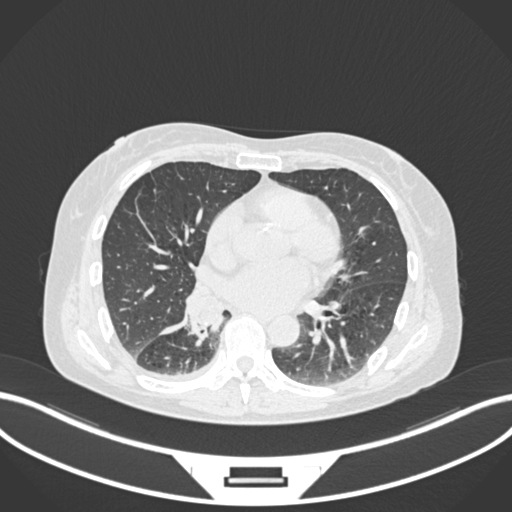
Chest CT, one axial slice. Slice 74 of 168 in the series (ordered by position). Reconstruction kernel B30f. 120 kVp. Lung window (W 1500 / L -600 HU). 512 × 512 image matrix, field of view 400 × 400 mm. Patient: female, 63 years. From the clinical record (not read from this slice): clinical TNM (as recorded): T1c N0 M0.
Annotated regions visible in this slice (bounding box drawn by a radiologist):
- lung tumour (recorded histology: adenocarcinoma): box from (x=184, y=290) to (x=226, y=344) px